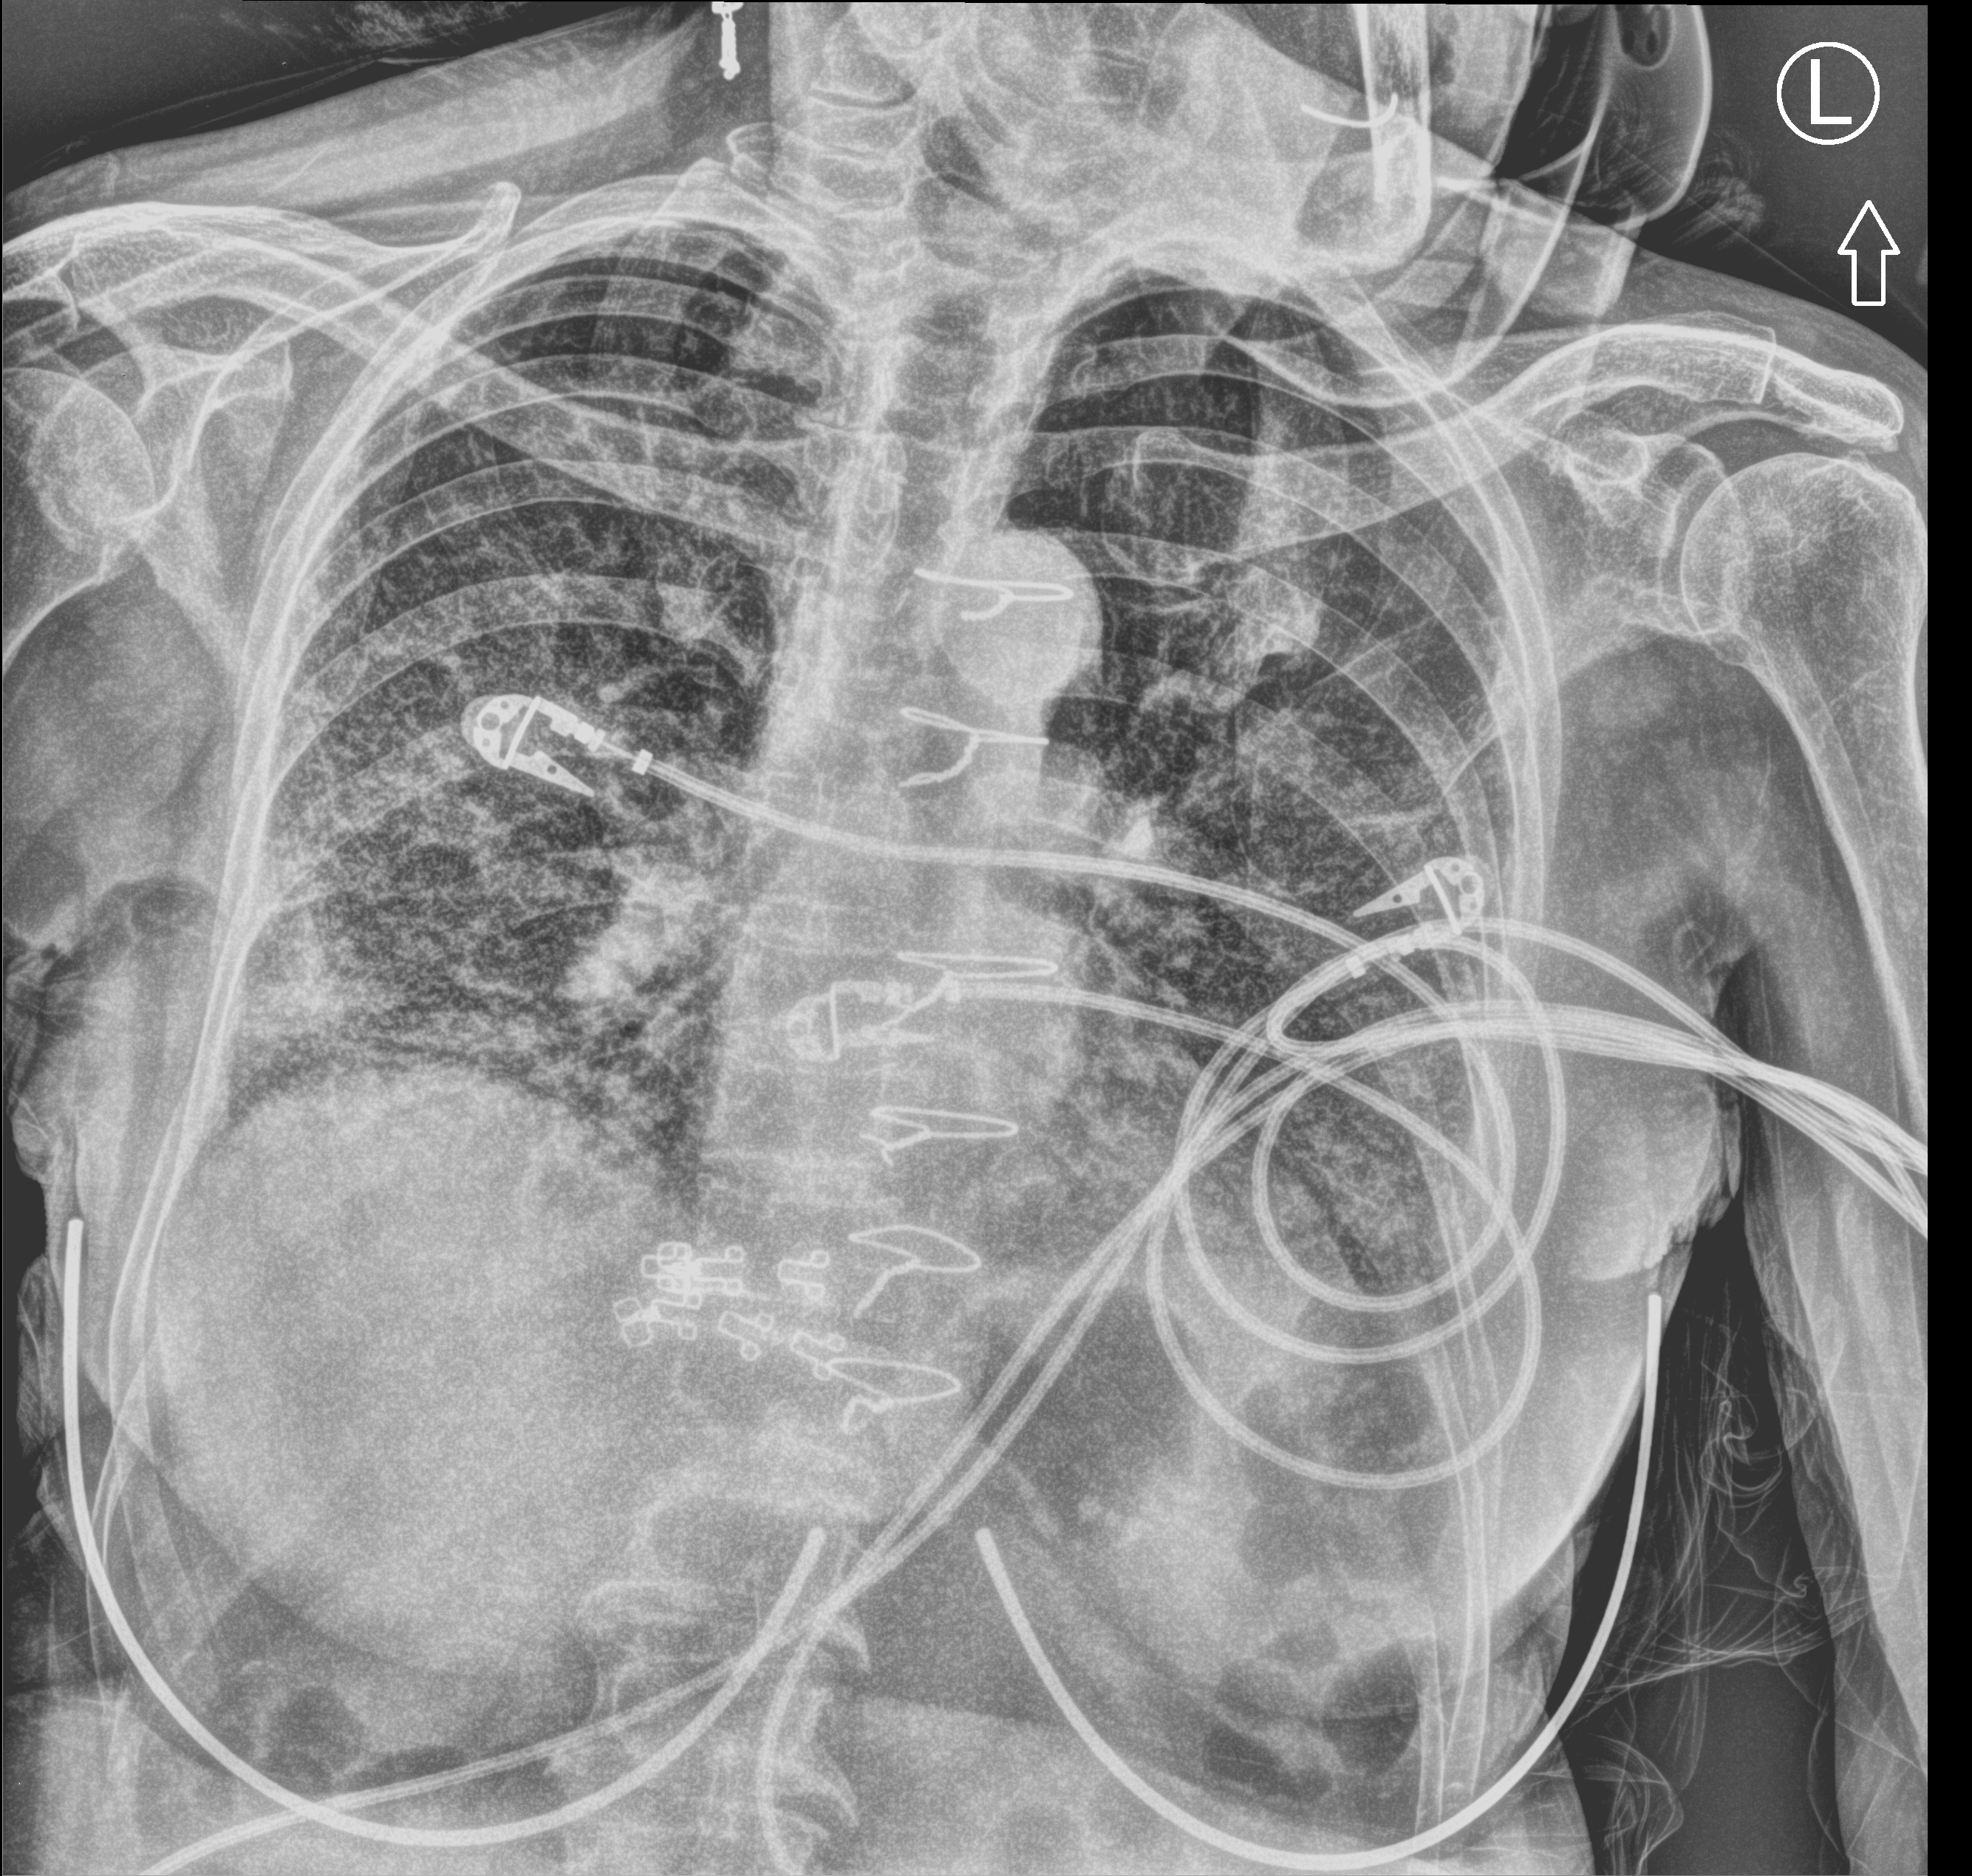
Chest X-ray (portable), anteroposterior (AP) projection. Female patient hospitalised with COVID-19, age 75–90 years.
From the hospital-stay record, not from the radiograph (when in the stay this image was taken is not recorded): length of hospital stay: 11 days.